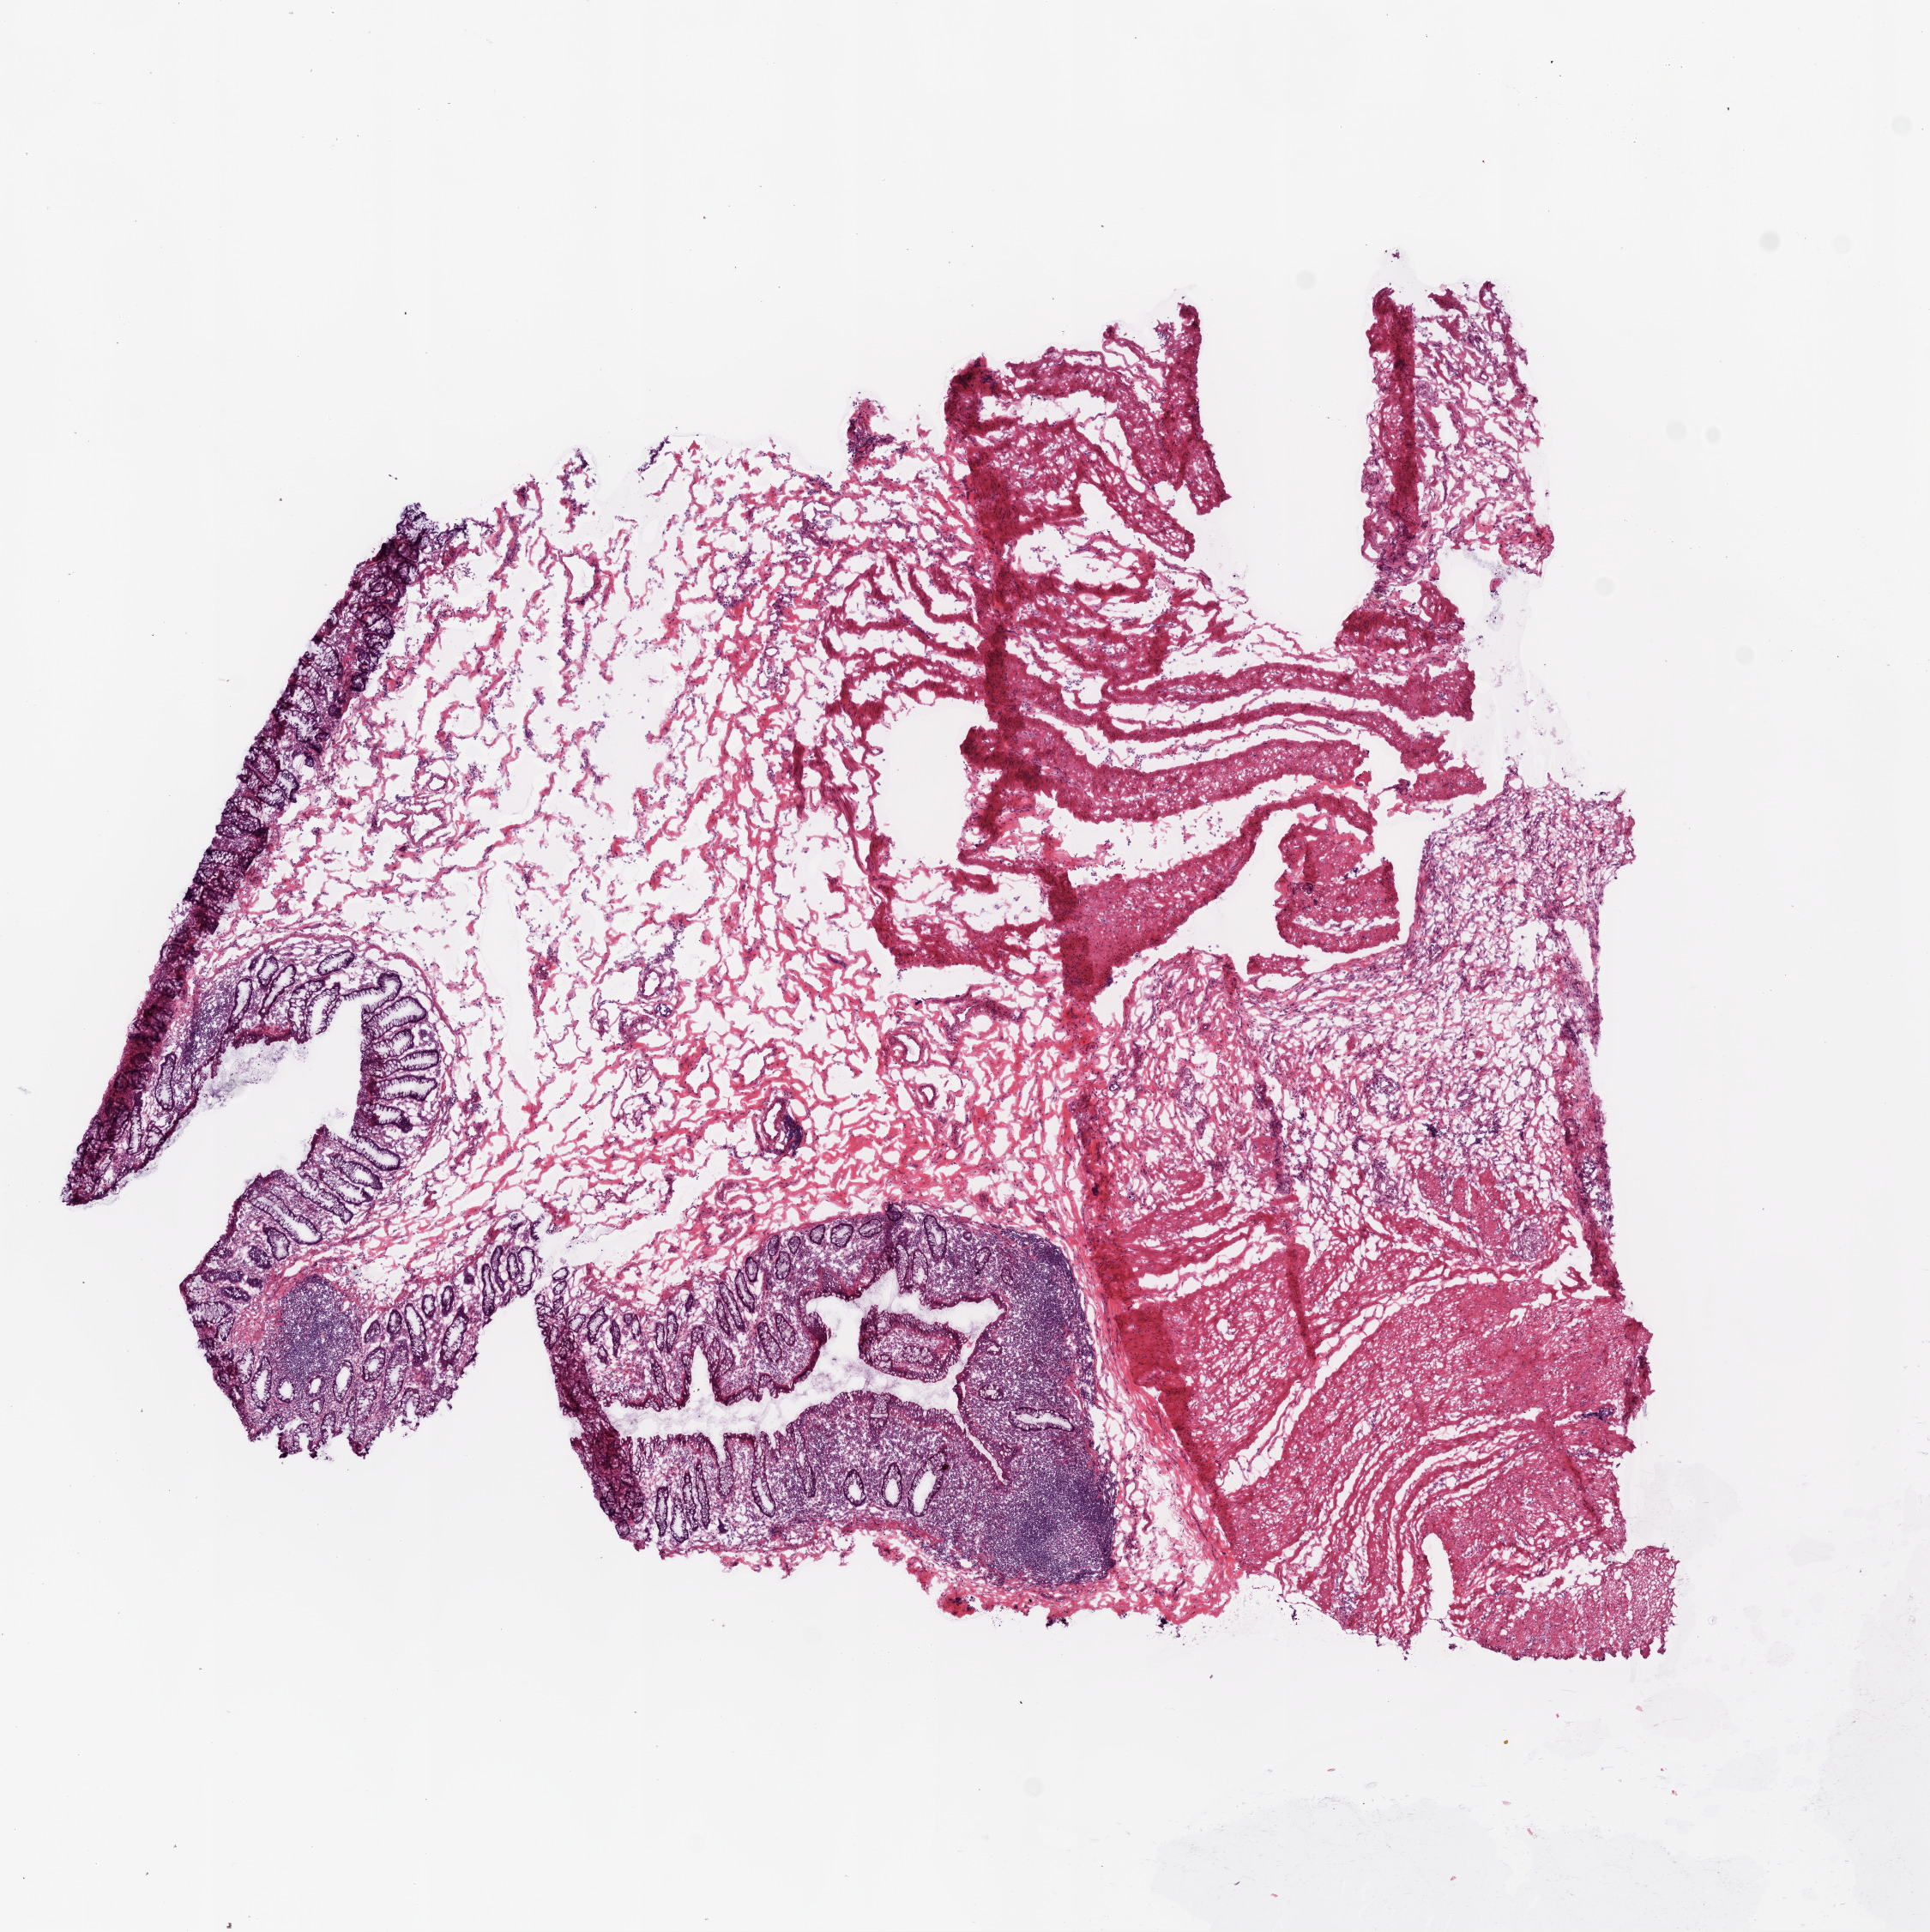
Digitized H&E-stained tissue section (whole slide), whole scanned area (about 9.0 x 9.0 mm, slide scanned at 20x) shown as a low-resolution overview, frozen section from the top of the tissue portion, ovary, solid tissue normal (non-tumour tissue) sample. Female patient; age at initial diagnosis 76 years.
This section: solid tissue normal (non-tumour) sample from the same patient. Patient diagnosis: Serous cystadenocarcinoma, NOS.